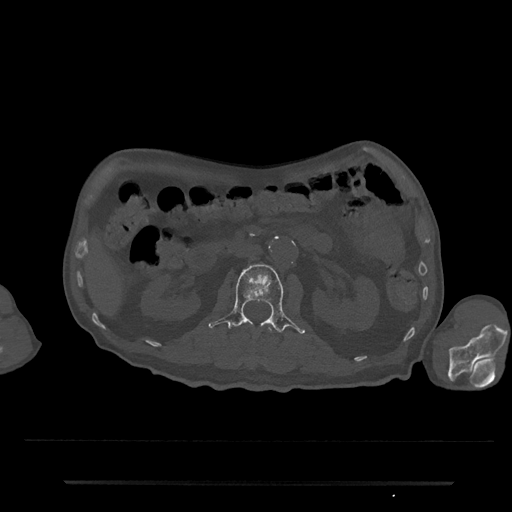
CT including the spine, one axial slice. Position 74 of 797 along the scan axis. Reconstruction kernel Br40s/3. Bone window (W 1800 / L 400 HU). 0.5 mm slice thickness. 512 × 512 image matrix, field of view 427 × 427 mm. Patient: male, 74 years. Case-level facts recorded for this patient, not image findings: primary cancer: prostate.
Structures marked on this image (semi-automatically segmented with operator editing):
- L1 vertebra: bounding box (x1, y1, x2, y2) in pixels: (250, 325, 273, 362)
- L2 vertebra: (209, 264, 305, 335)